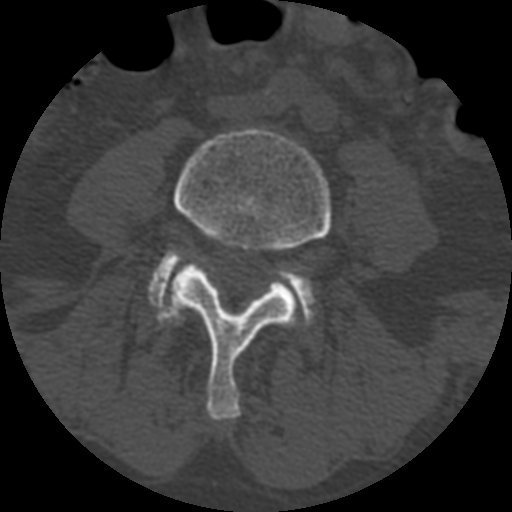
CT including the spine, one axial slice; slice 276 of 399 in the series (ordered by position); 120 kVp; bone window (W 1800 / L 400 HU); 512 × 512 image matrix, field of view 160 × 160 mm. Patient age 71 years. From the clinical record (not read from this slice): primary cancer: prostate.
Outlined on this slice (semi-automatically segmented with operator editing):
- L4 vertebra: box from (x=159, y=129) to (x=331, y=420) px
- L5 vertebra: (x=147, y=250)–(x=317, y=326)